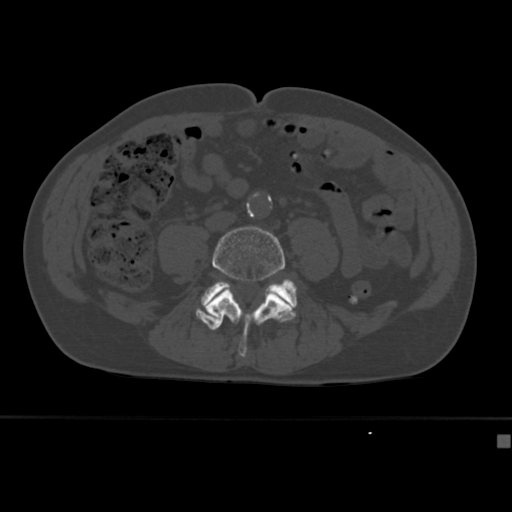
CT including the spine, one axial slice. Slice 101 of 430 in the series (ordered by position). Bone window (W 1800 / L 400 HU). 1.5 mm slice thickness. 512 × 512 image matrix. Patient: male, 64 years. Case-level facts recorded for this patient, not image findings: primary cancer: uterus; vertebrae with lytic lesions (as recorded): T1, T4, T5, T7, L5.
Outlined on this slice (semi-automatic segmentation, software-assisted and operator-edited):
- L4 vertebra: bounding box <205,226,292,357> (left, top, right, bottom; pixels)
- L5 vertebra: <201,280,298,324>